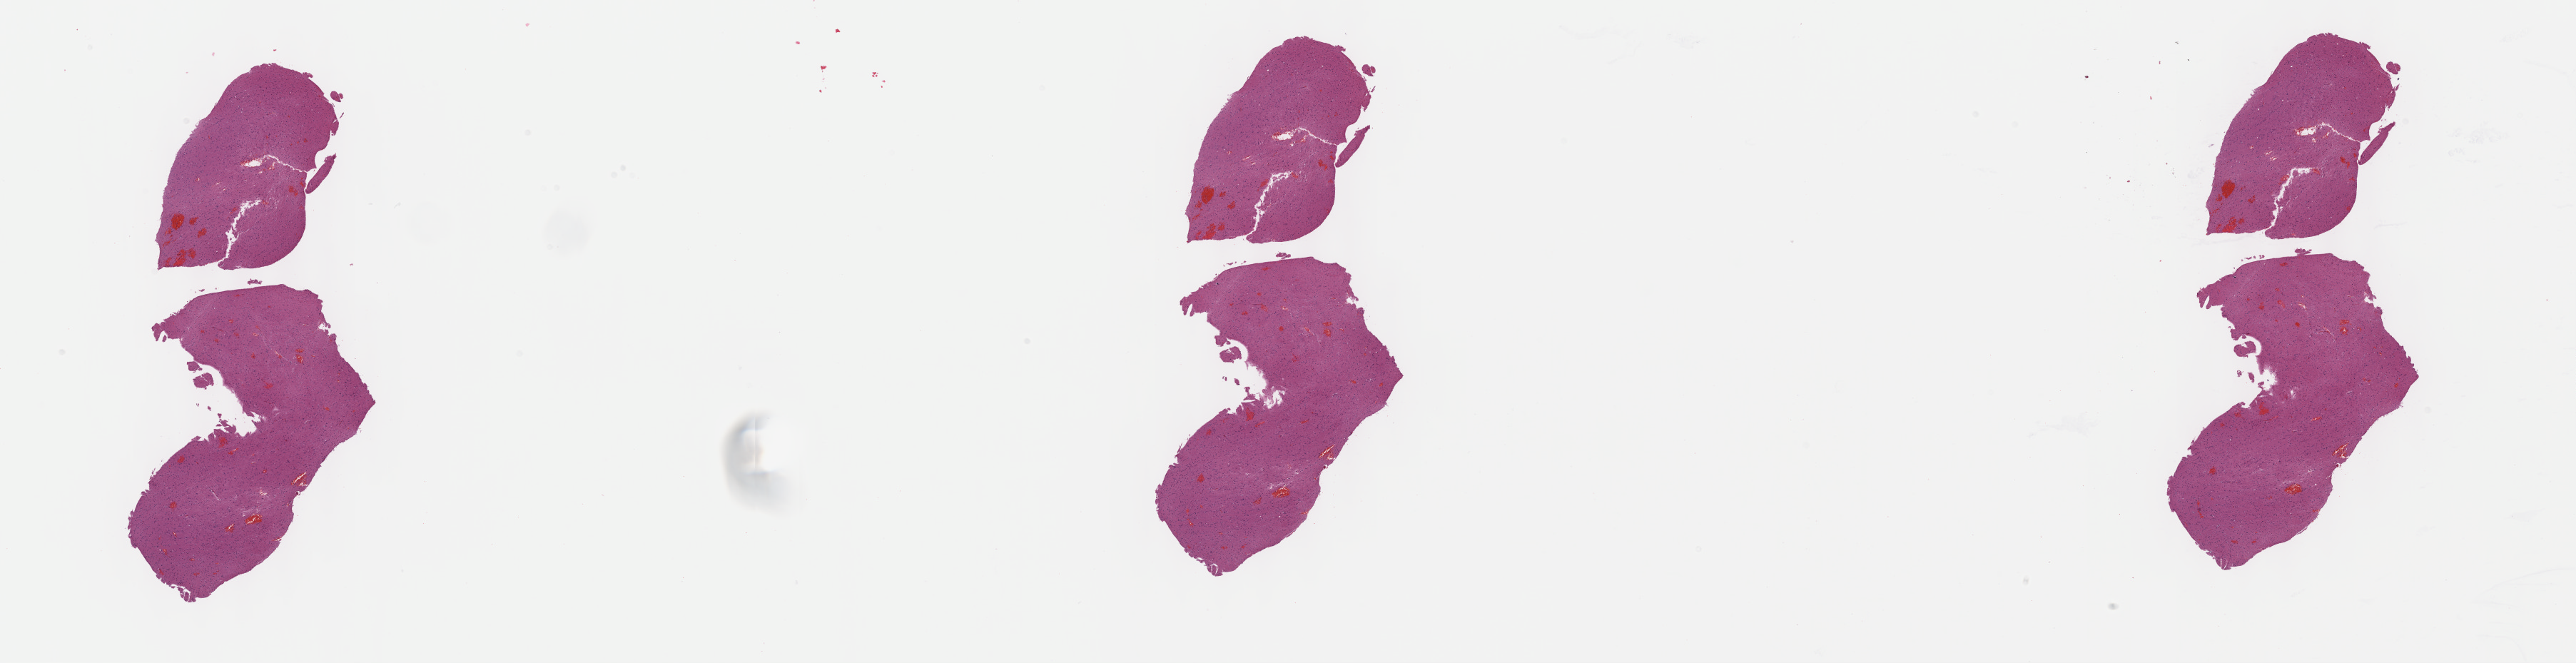
Whole-slide histology image, H&E-stained, shown as a low-resolution overview of the whole scanned area (about 29.2 x 7.5 mm). Formalin-fixed paraffin-embedded (FFPE) diagnostic section. Sample: primary tumour, brain. Patient: male, age at initial diagnosis 38 years. Histologic grade: G2 (moderately differentiated).
Pathologic diagnosis: Oligodendroglioma, NOS.